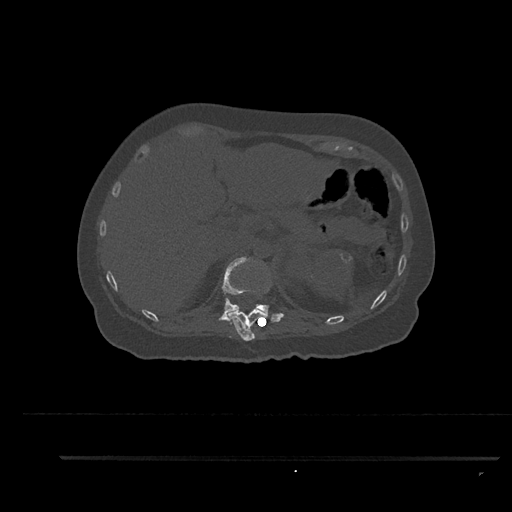
CT including the spine, one axial slice. Position 290 of 797 along the scan axis. 120 kVp. Bone window (W 1800 / L 400 HU). 0.5 mm slice thickness. 512 × 512 image matrix, field of view 408 × 408 mm. Female patient, age 44 years. From the clinical record (not read from this slice): primary cancer: renal; vertebrae with lytic lesions (as recorded): L1.
Outlined on this slice (semi-automatically segmented with operator editing):
- T11 vertebra: bounding box <229,308,267,341> (left, top, right, bottom; pixels)
- T12 vertebra: <218,257,284,323>